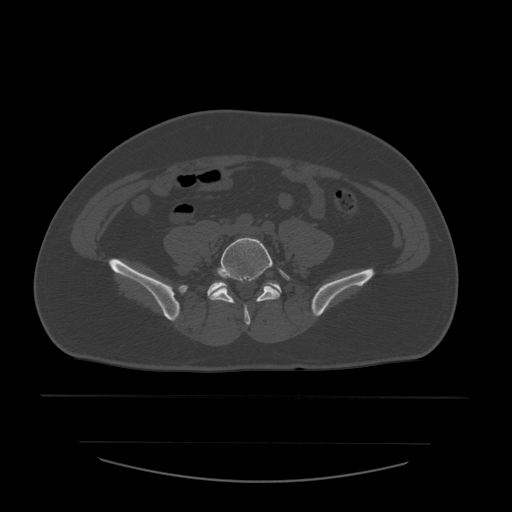
CT including the spine, one axial slice. Slice 116 of 532 in the series (ordered by position). Reconstruction kernel STANDARD. Bone window (W 1800 / L 400 HU). 1.25 mm slice thickness. 512 × 512 image matrix. Patient age 44 years. From the clinical record (not read from this slice): primary cancer: soft tissue sarcoma.
Outlined on this slice (semi-automatic segmentation, software-assisted and operator-edited):
- L5 vertebra: bounding box (x1, y1, x2, y2) in pixels: (208, 237, 290, 326)